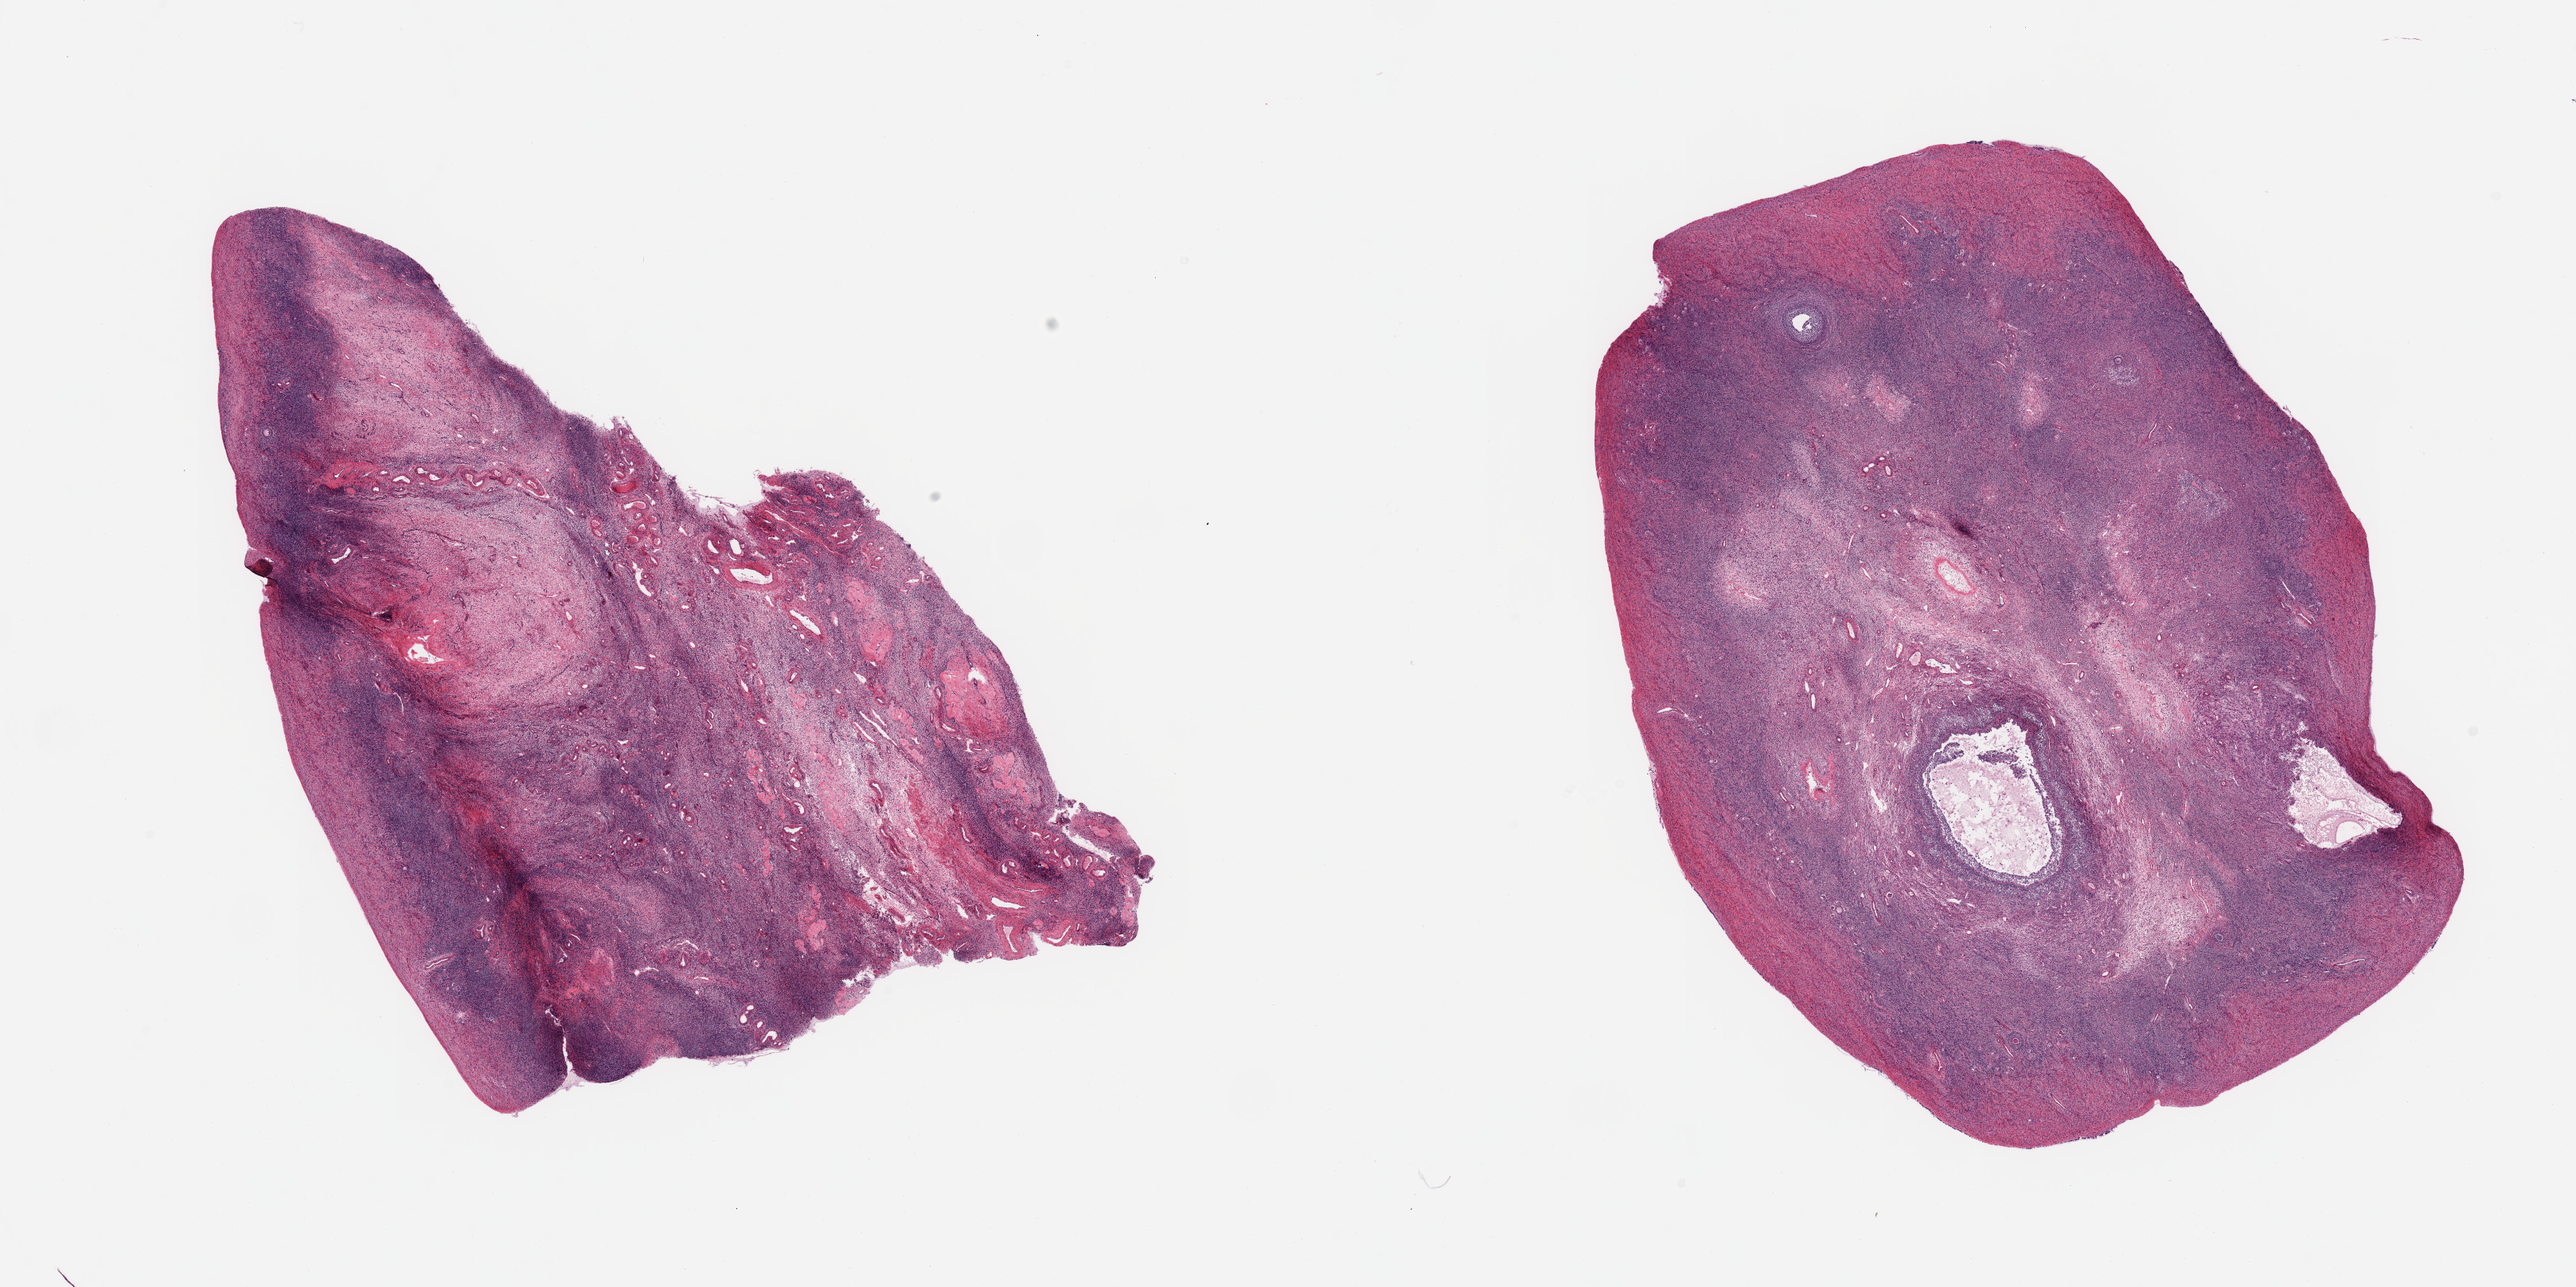
Digitized hematoxylin and eosin (H&E)-stained section, whole scanned area (about 25.6 x 12.8 mm) shown as a low-resolution overview; PAXgene-fixed, paraffin-embedded tissue; target tissue: ovary; donor tissue sample. Donor sex: female.
- reviewer comment on this tissue sample: 2 pieces; many follicles, corpora albicanta and lutea in different stages of development